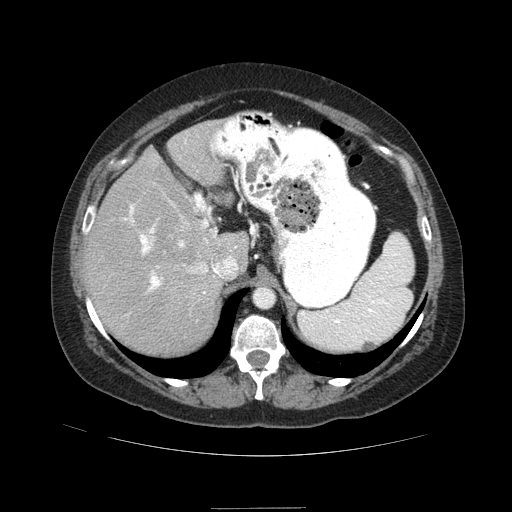
Contrast-enhanced abdominal CT (liver protocol), one axial slice; slice 61 of 89 in the series (ordered by position); 120 kVp; soft-tissue window (W 400 / L 40 HU); 512 × 512 image matrix. Case-level facts recorded for this patient, not image findings: diagnosis: hepatocellular carcinoma (patient treated with transarterial chemoembolisation; whether this scan precedes or follows treatment is not stated here); TNM stage (as recorded): Stage-IIIB; Child-Pugh class: A; tumour nodularity: multinodular.
Annotated regions visible in this slice (semi-automatically segmented with operator editing):
- abdominal aorta: box from (x=254, y=287) to (x=274, y=307) px
- liver parenchyma outside the tumour (the mass and vessels are separate outlines, so this box may not span the whole liver): (x=82, y=120)–(x=250, y=356)
- liver vessels: (x=88, y=141)–(x=237, y=294)